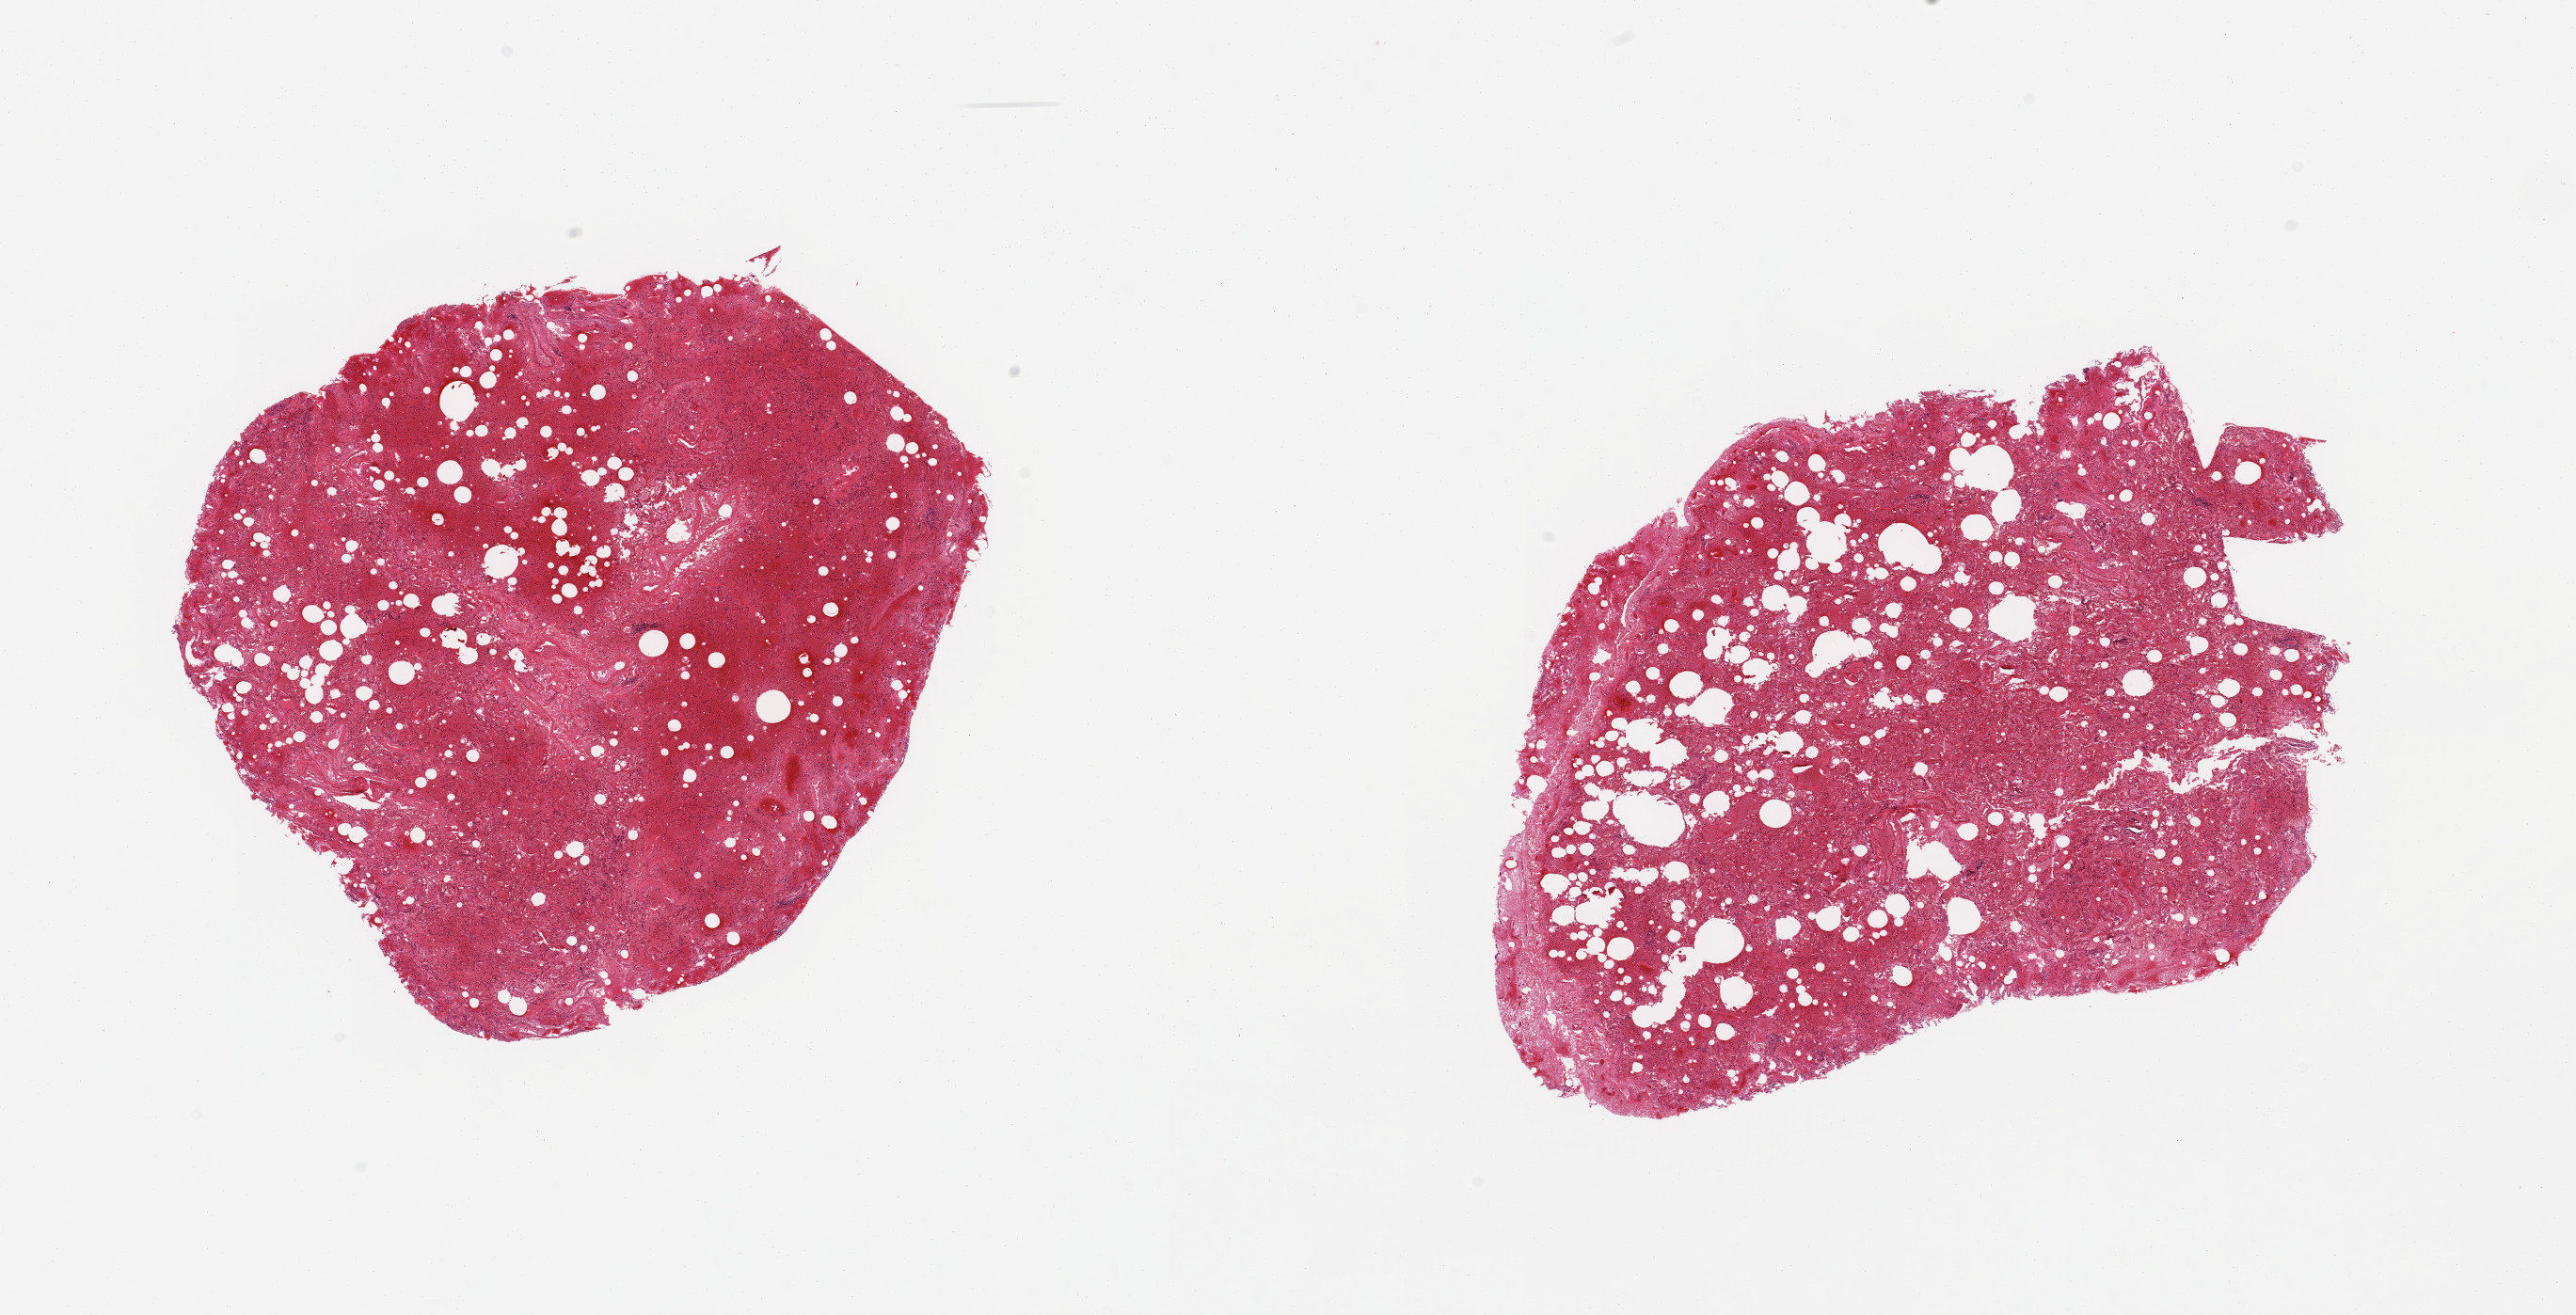
Whole-slide image, H&E stain, shown as a low-resolution overview of the whole scanned area (about 21.7 x 11.1 mm). PAXgene-fixed paraffin-embedded (PFPE) section. Target tissue: lung. Donor tissue sample.
Reviewer comment on this tissue sample: 2 pieces; severe congestion and pulmonary hemorrhage.